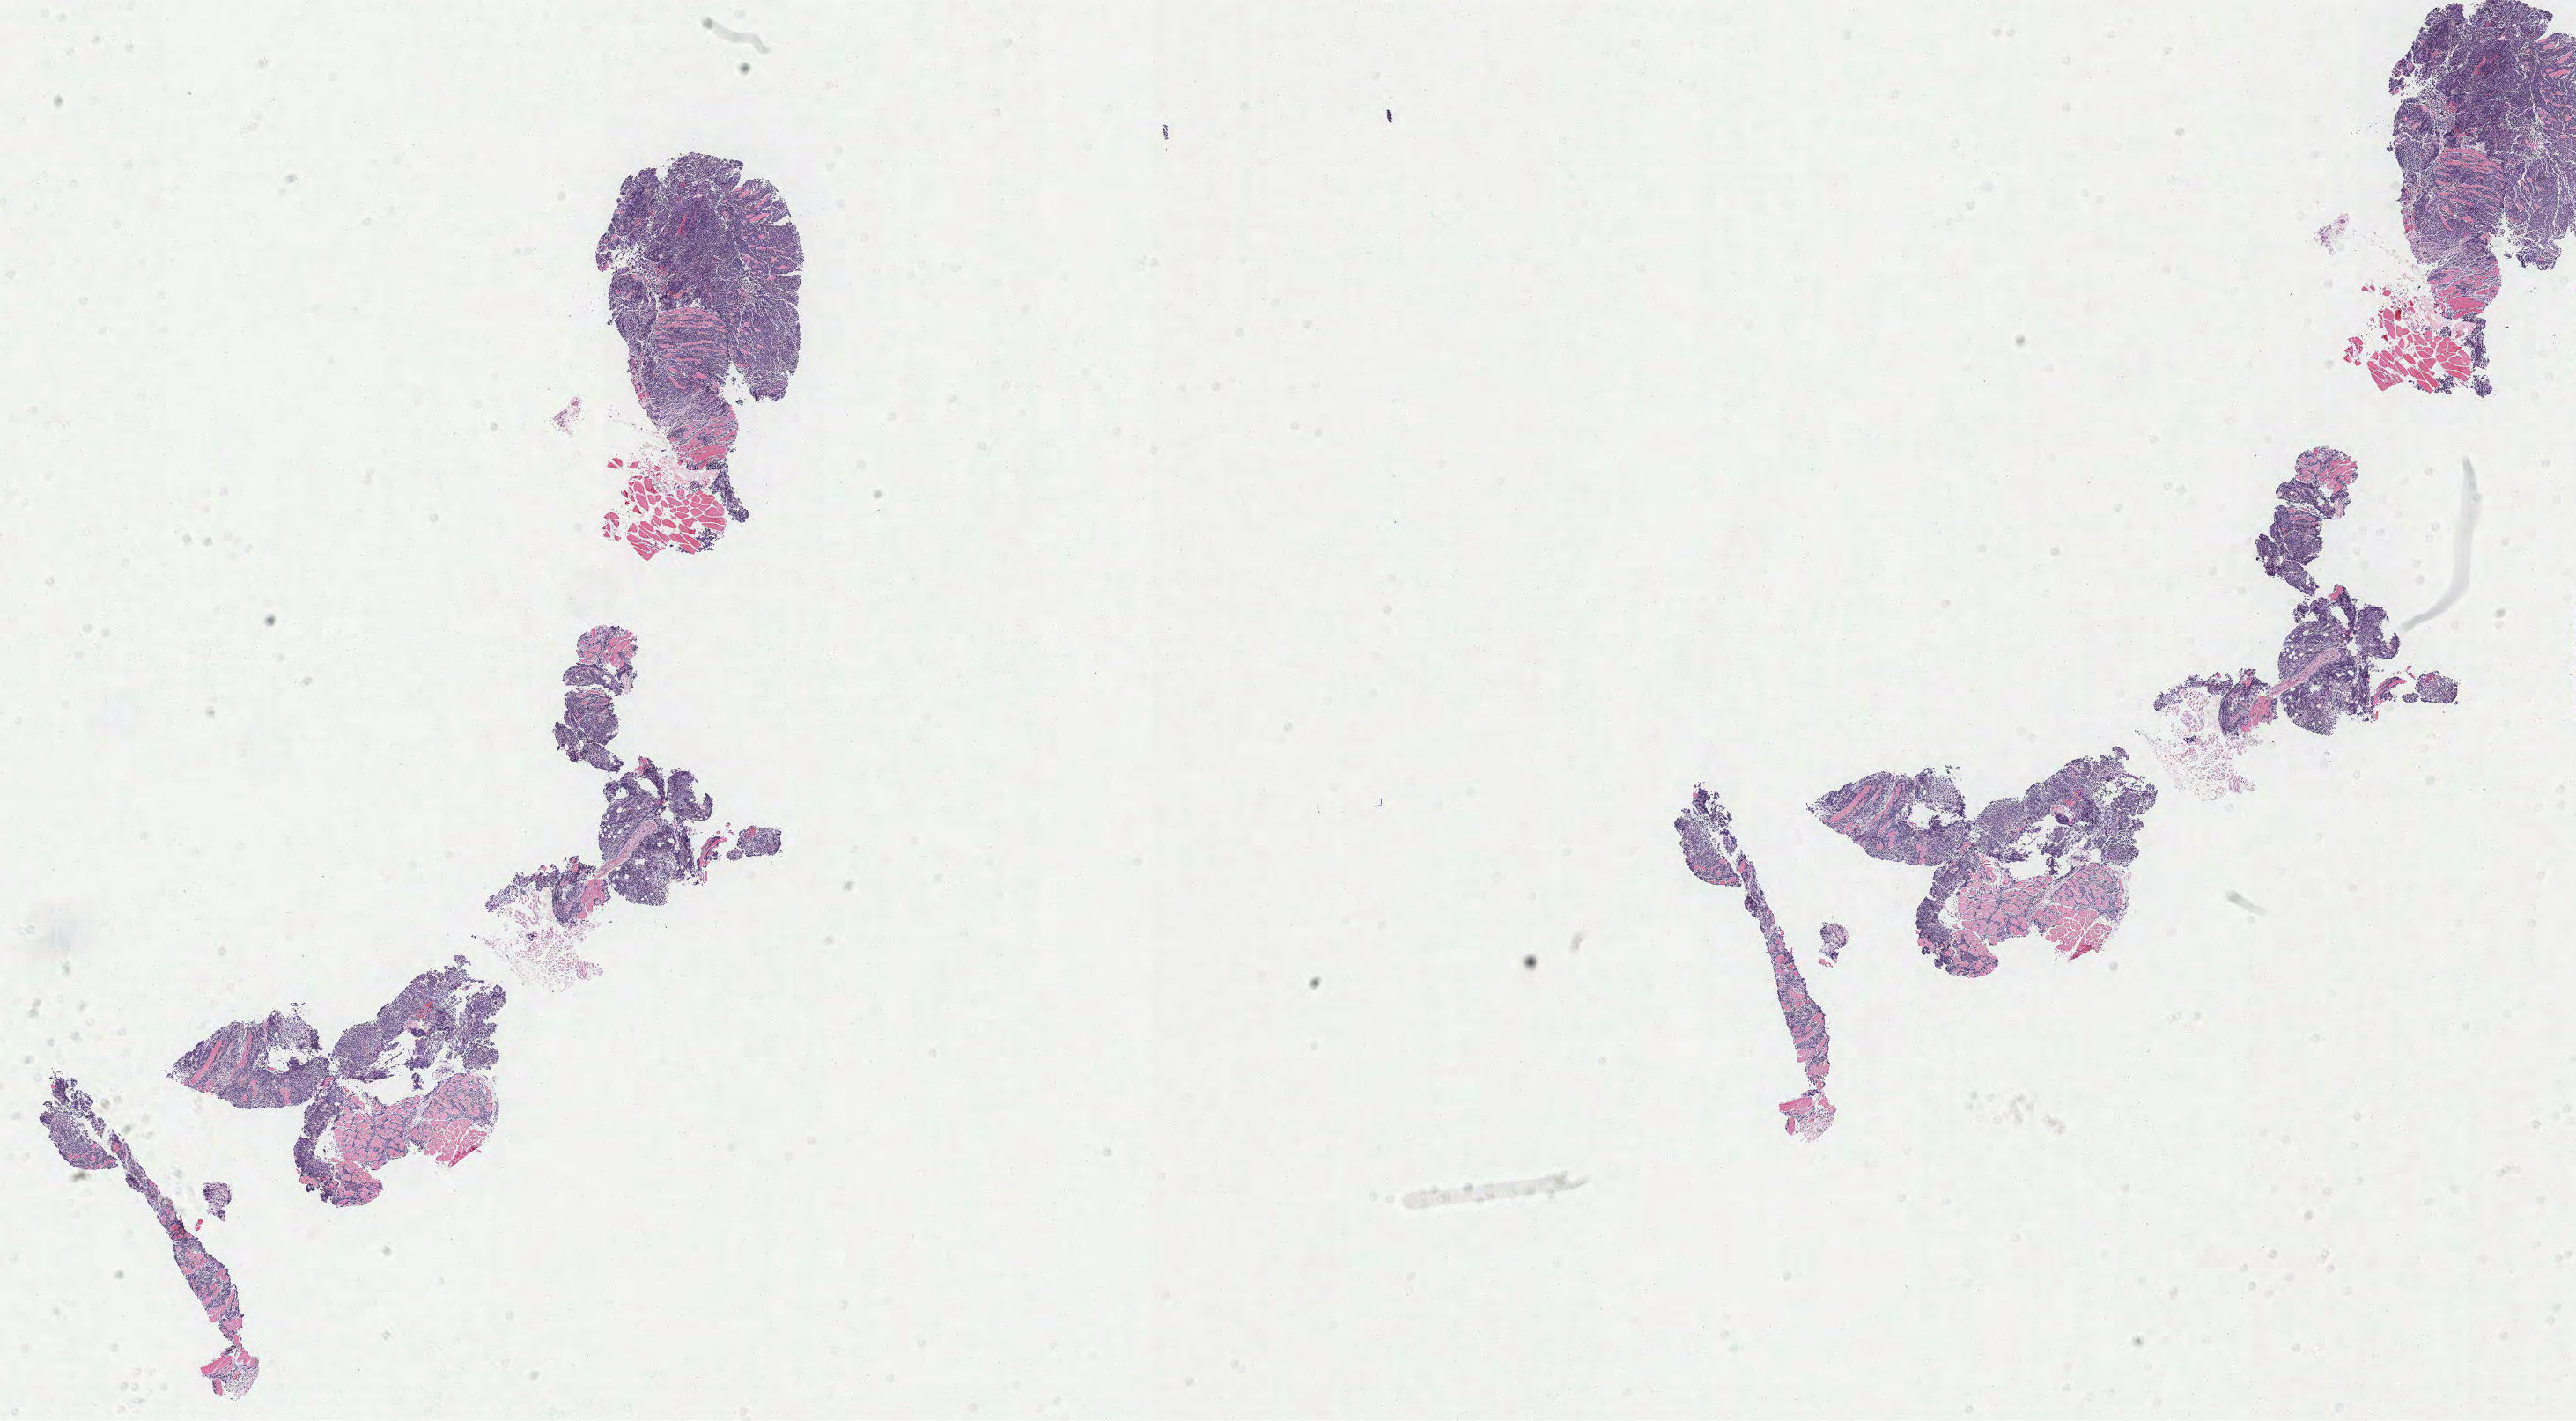
Whole-slide image, haematoxylin and eosin stain, a low-resolution overview of the entire scanned area, about 23.2 x 12.8 mm. Specimen: tumor tissue. Patient: female, aged 69.
- histologic diagnosis: Burkitt lymphoma, NOS